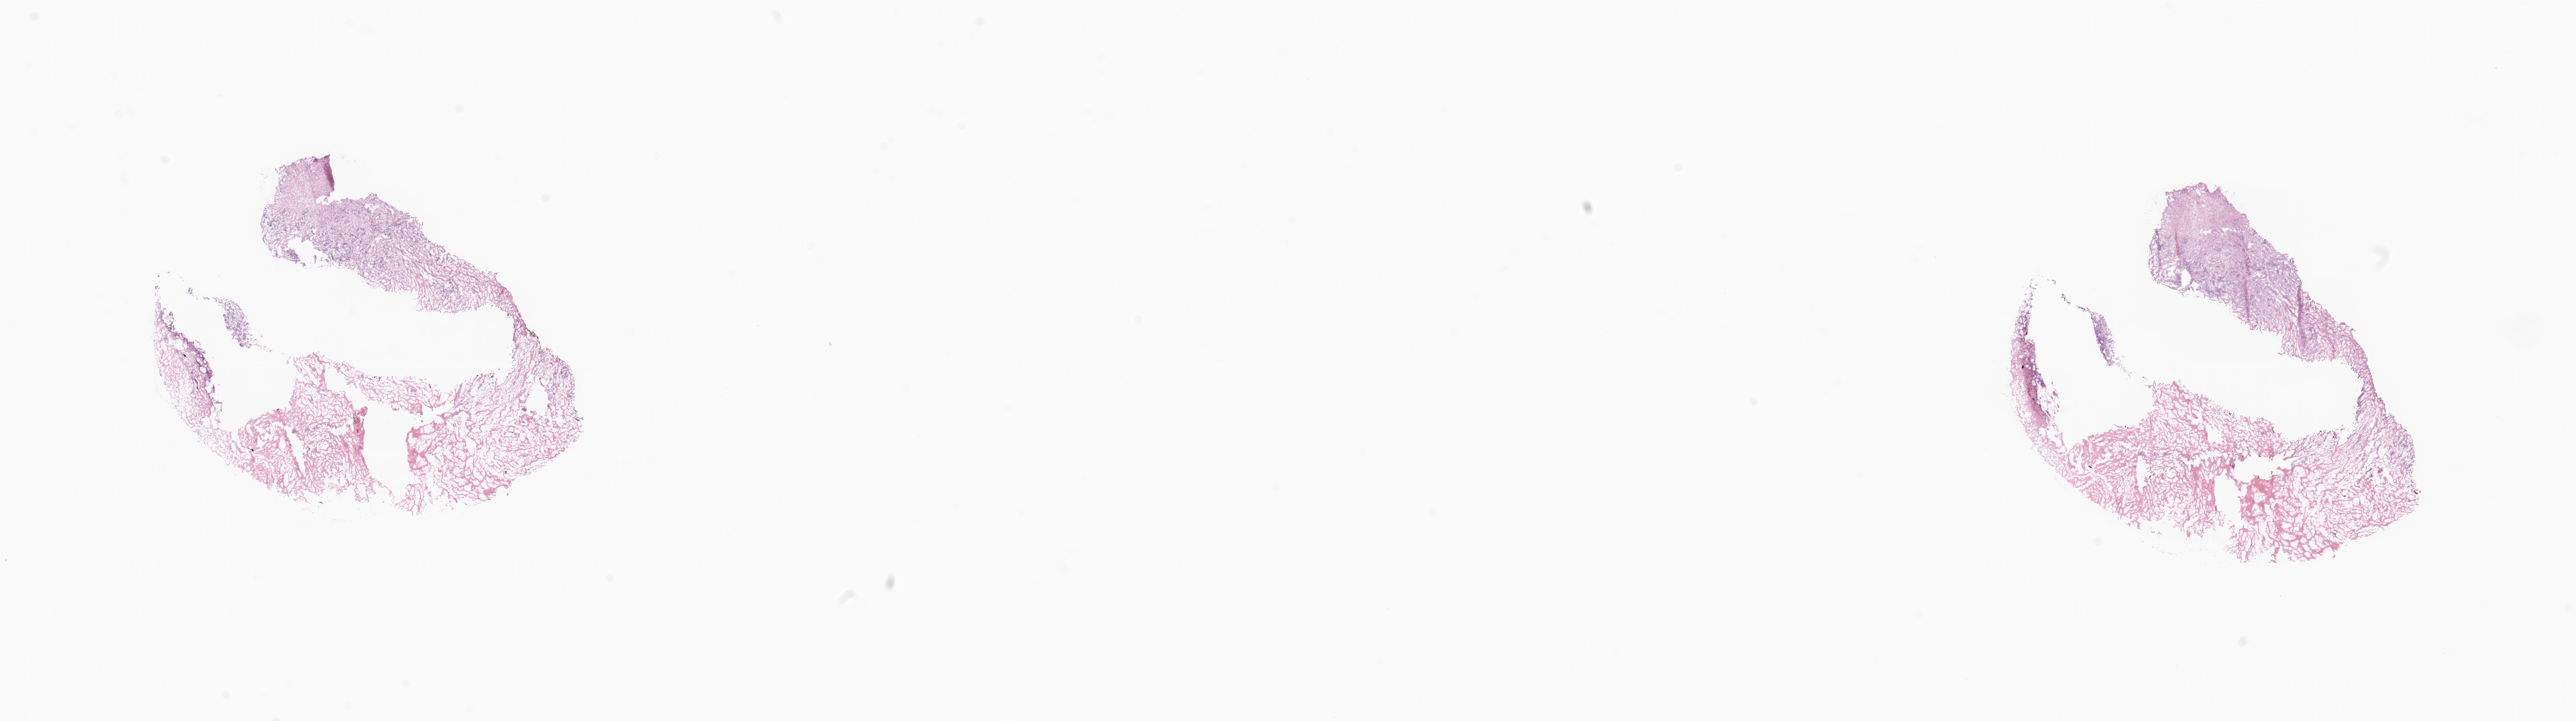
Whole-slide image, haematoxylin and eosin stain, a low-resolution overview of the entire scanned area, about 30.6 x 8.6 mm. Frozen section. Specimen: primary tumor. Anatomic site: breast (right). Female patient; age at initial diagnosis 89 years. Slide review estimates, as recorded: tumor cells 17%, tumor nuclei 59%.
Diagnosis: Infiltrating duct carcinoma, NOS.